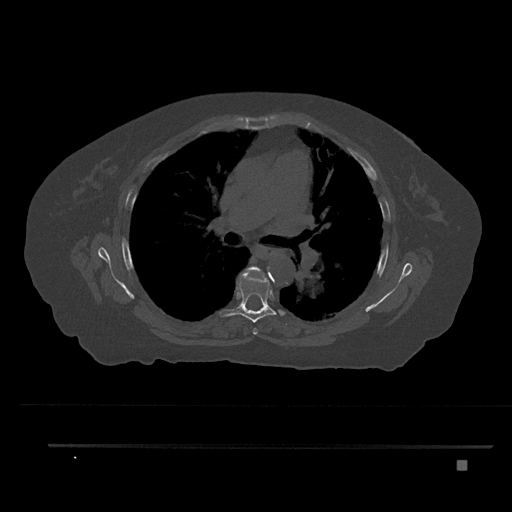
CT including the spine, one axial slice; position 533 of 797 along the scan axis; 120 kVp; bone window (W 1800 / L 400 HU); 512 × 512 image matrix, field of view 437 × 437 mm. Patient: female, 76 years. From the clinical record (not read from this slice): primary cancer: lung.
Outlined on this slice (semi-automatically segmented with operator editing):
- T5 vertebra: box from (x=245, y=266) to (x=269, y=335) px
- T6 vertebra: (x=219, y=272)–(x=285, y=322)